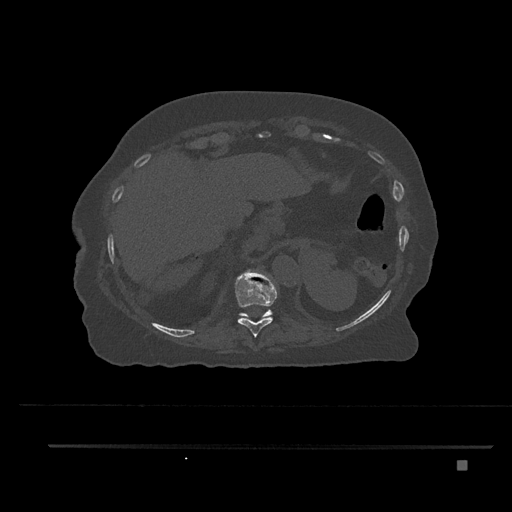
CT including the spine, one axial slice; slice 345 of 797 in the series (ordered by position); 120 kVp; bone window (W 1800 / L 400 HU); 512 × 512 image matrix. Female patient, age 76 years. From the clinical record (not read from this slice): primary cancer: lung.
Annotated regions visible in this slice (semi-automatically segmented with operator editing):
- T10 vertebra: box from (x=235, y=272) to (x=278, y=337) px
- T11 vertebra: (x=239, y=310)–(x=272, y=319)